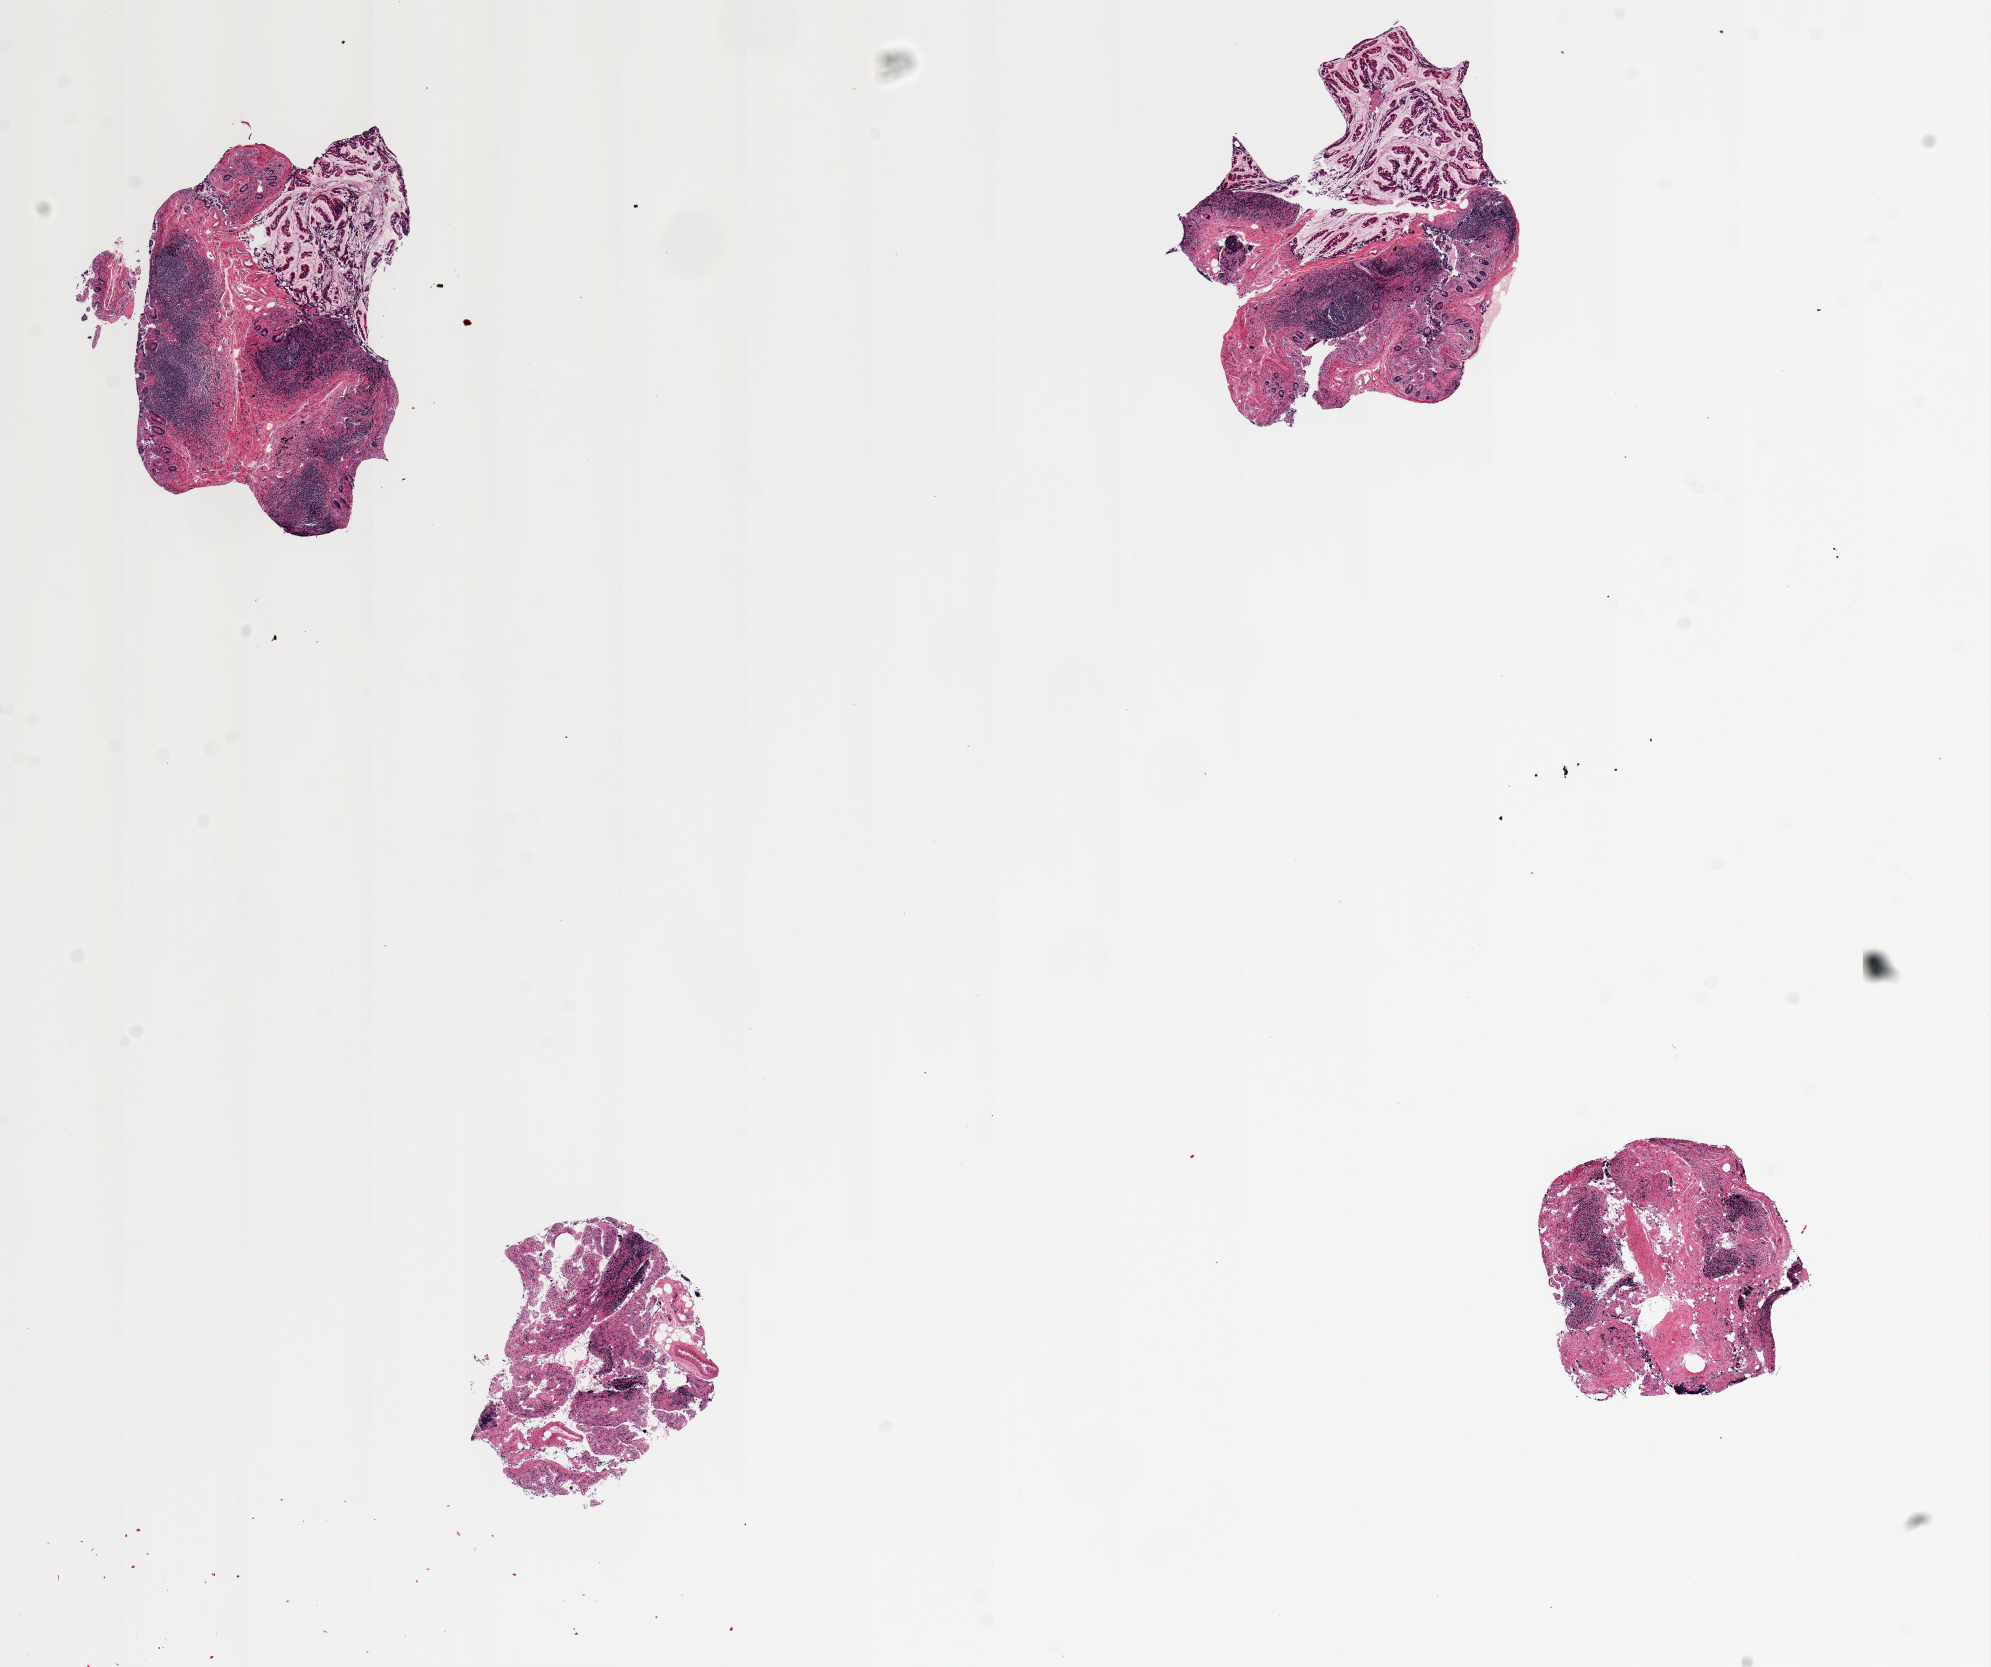
Digitized hematoxylin and eosin (H&E)-stained section, low-resolution overview of the scanned area, about 15.8 x 13.2 mm. PAXgene-fixed paraffin-embedded (PFPE) section. Target tissue: ileum. Tissue donor sample. Male donor.
• pathologist's review note for this sample: 4 pieces, up to 3x3mm; good specimens, ~30% total are lymphoid aggregates